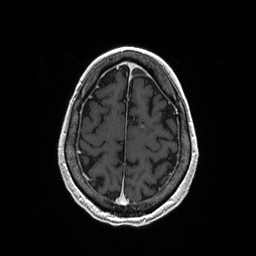
Brain MRI from a brain-tumour surgery series, one axial slice; position 57 of 208 along the scan axis; T1-weighted post-contrast; 256 × 256 image matrix, field of view 256 × 256 mm. From the clinical record (not read from this slice): histopathology: Primary diffuse large B-cell lymphoma; tumour location: Left Corpus Callosum (Frontal).
Outlined on this slice (outlined manually by an expert reader):
- tumour: bounding box [x1, y1, x2, y2] px = [141, 125, 144, 128]